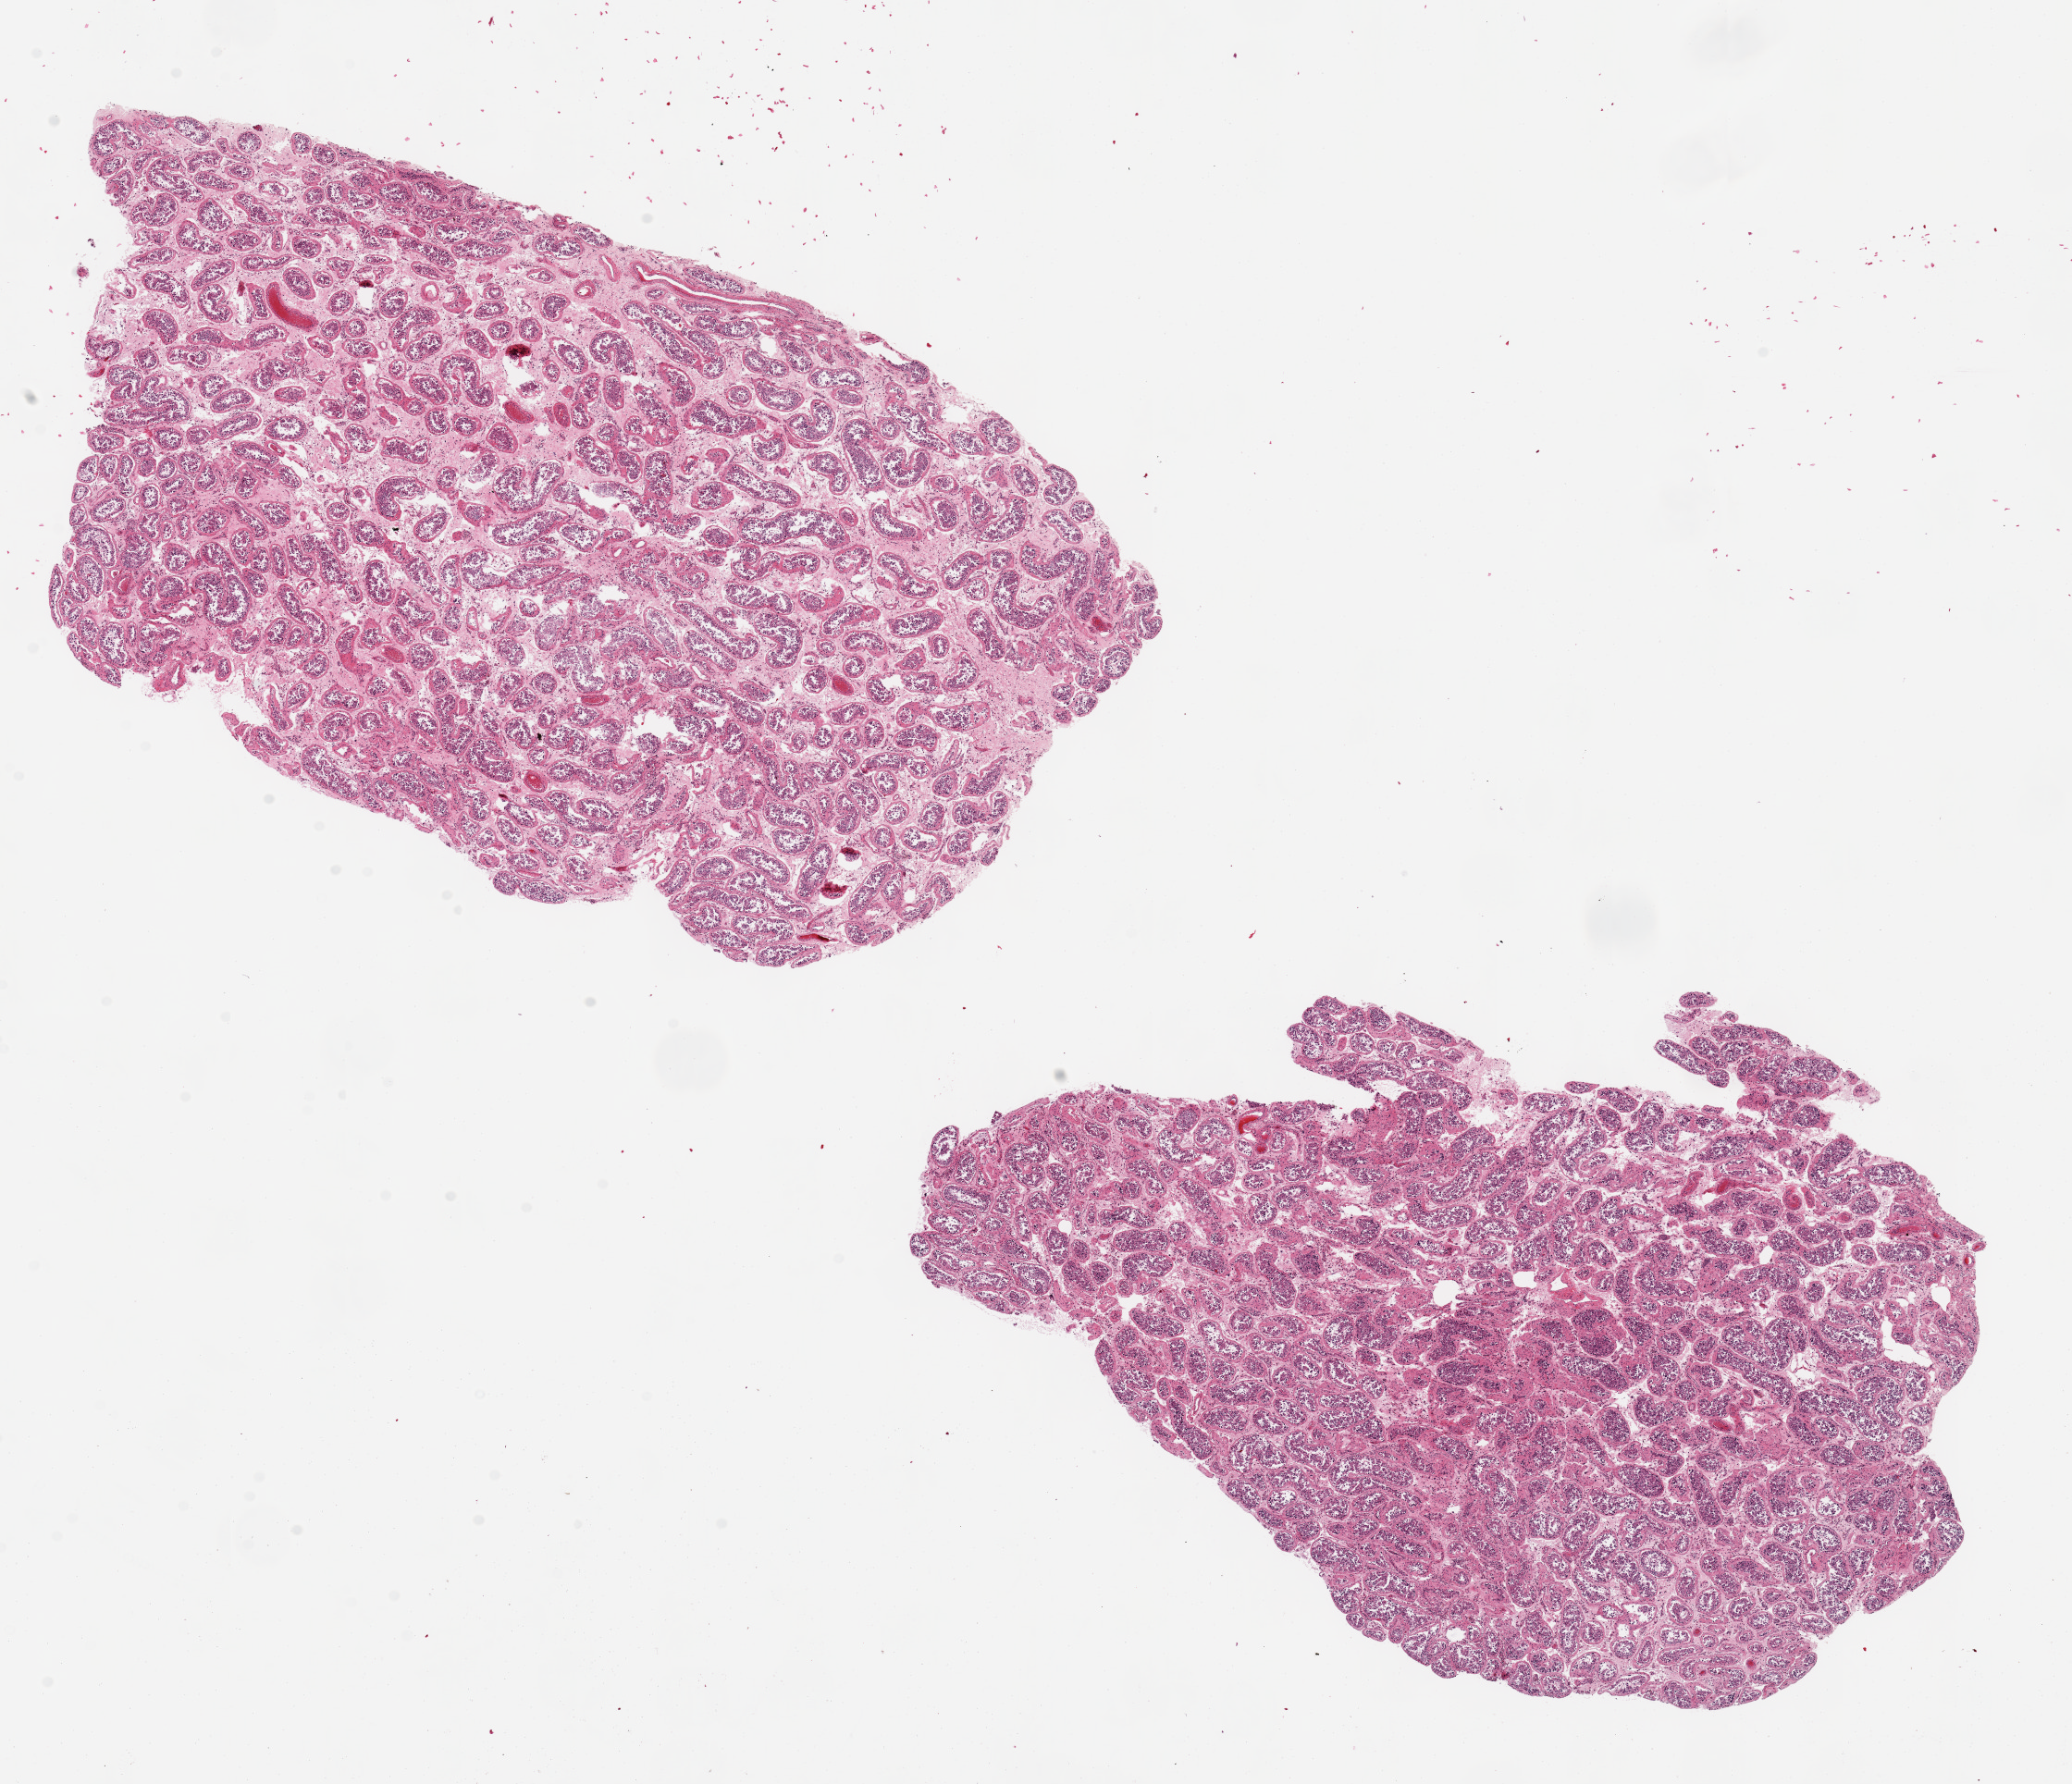
Whole-slide image, haematoxylin and eosin stain, a low-resolution overview of the entire scanned area, about 17.7 x 15.3 mm (acquisition: 20x scan), PAXgene-fixed paraffin-embedded (PFPE) section, sampled site (target tissue): testis, tissue donor sample. Donor sex: male.
Pathologist's review note for this sample: 2 `9.5x6.5mm aliquots. Markedly reduced spermatogenesis.